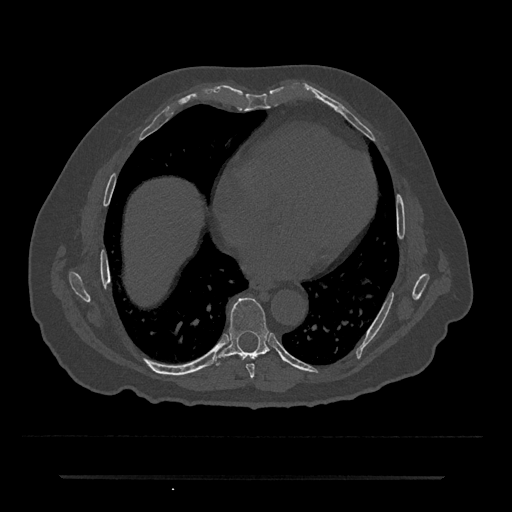
CT including the spine, one axial slice; position 348 of 797 along the scan axis; reconstruction kernel Br40s/3; 120 kVp; bone window (W 1800 / L 400 HU); 0.5 mm slice thickness; 512 × 512 image matrix, field of view 437 × 437 mm. Male patient, age 69 years. From the clinical record (not read from this slice): primary cancer: prostate.
Structures marked on this image (semi-automatic segmentation, software-assisted and operator-edited):
- T7 vertebra: bounding box [x1, y1, x2, y2] px = [246, 364, 255, 378]
- T8 vertebra: [214, 298, 270, 366]